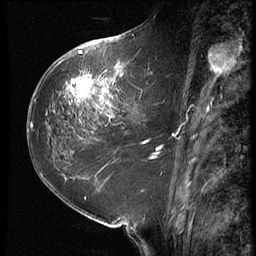
Breast MRI (dynamic contrast-enhanced), one sagittal slice; position 30 of 64 along the scan axis; 3 images stored at this slice position (order not interpretable as contrast timing); 1.5 T; TE 4.2 ms, TR 9 ms; 2.5 mm slice thickness; 256 × 256 image matrix, field of view 180 × 180 mm. Patient: female, 59 years. Case-level facts recorded for this patient, not image findings: setting: breast cancer imaged before/during neoadjuvant chemotherapy; receptor status: HER2-positive.
Outlined on this slice (semi-automatically segmented with operator editing):
- analysis volume of interest (the breast-tissue region the enhancement analysis was run in; not a lesion): bounding box [x1, y1, x2, y2] px = [54, 65, 155, 132]
- tumour enhancement mask (voxels above the 140 % enhancement threshold inside the analysis volume of interest): [66, 65, 135, 117]